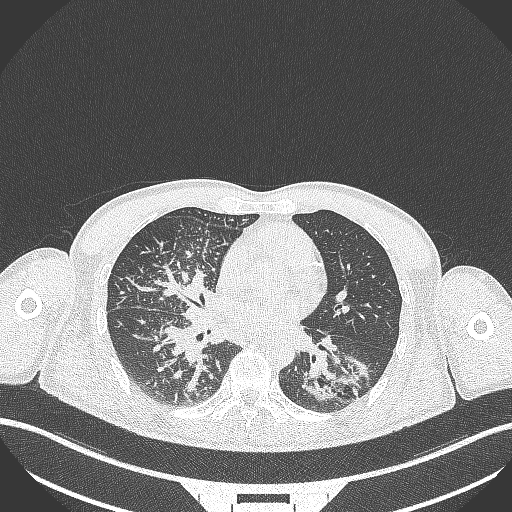
Chest CT, one axial slice. Lung window (W 1500 / L -600 HU). 512 × 512 image matrix, field of view 400 × 400 mm. Male patient, age 49 years. From the clinical record (not read from this slice): clinical TNM (as recorded): T2b N1 M0.
Structures marked on this image (bounding box drawn by a radiologist):
- lung tumour (recorded histology: adenocarcinoma): box from (x=298, y=357) to (x=364, y=409) px